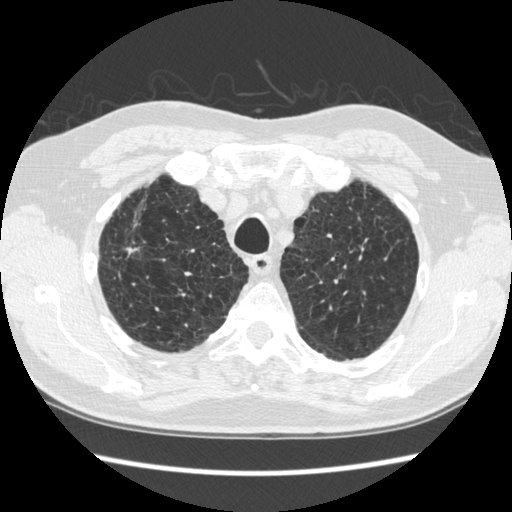
Axial slice from a low-dose chest CT screening exam, second screening round (one year after baseline), lung window (W 1500 / L -600 HU), 1.25 mm slice thickness. Male participant, aged 70 years at enrolment. Former smoker at enrolment.
- Expert reader's lesion annotation, bounding box (x1, y1, x2, y2) in pixels: (334, 210, 395, 278).
- The screening reader recorded 5 non-calcified nodules or masses ≥4 mm on this exam (right lower lobe, right lower lobe, right lower lobe, left upper lobe, left lower lobe); which of them this box marks is not recorded.
- Official screen result: positive, change unspecified: nodule(s) >= 4 mm or enlarging nodule(s), mass(es), or other non-specific abnormalities suspicious for lung cancer.
- Participant outcome: lung cancer diagnosed 479 days after this screen (after the third annual screen) — squamous cell carcinoma, NOS, left upper lobe, moderately differentiated (G2), stage IA (AJCC 6th edition), 18 mm at pathology.